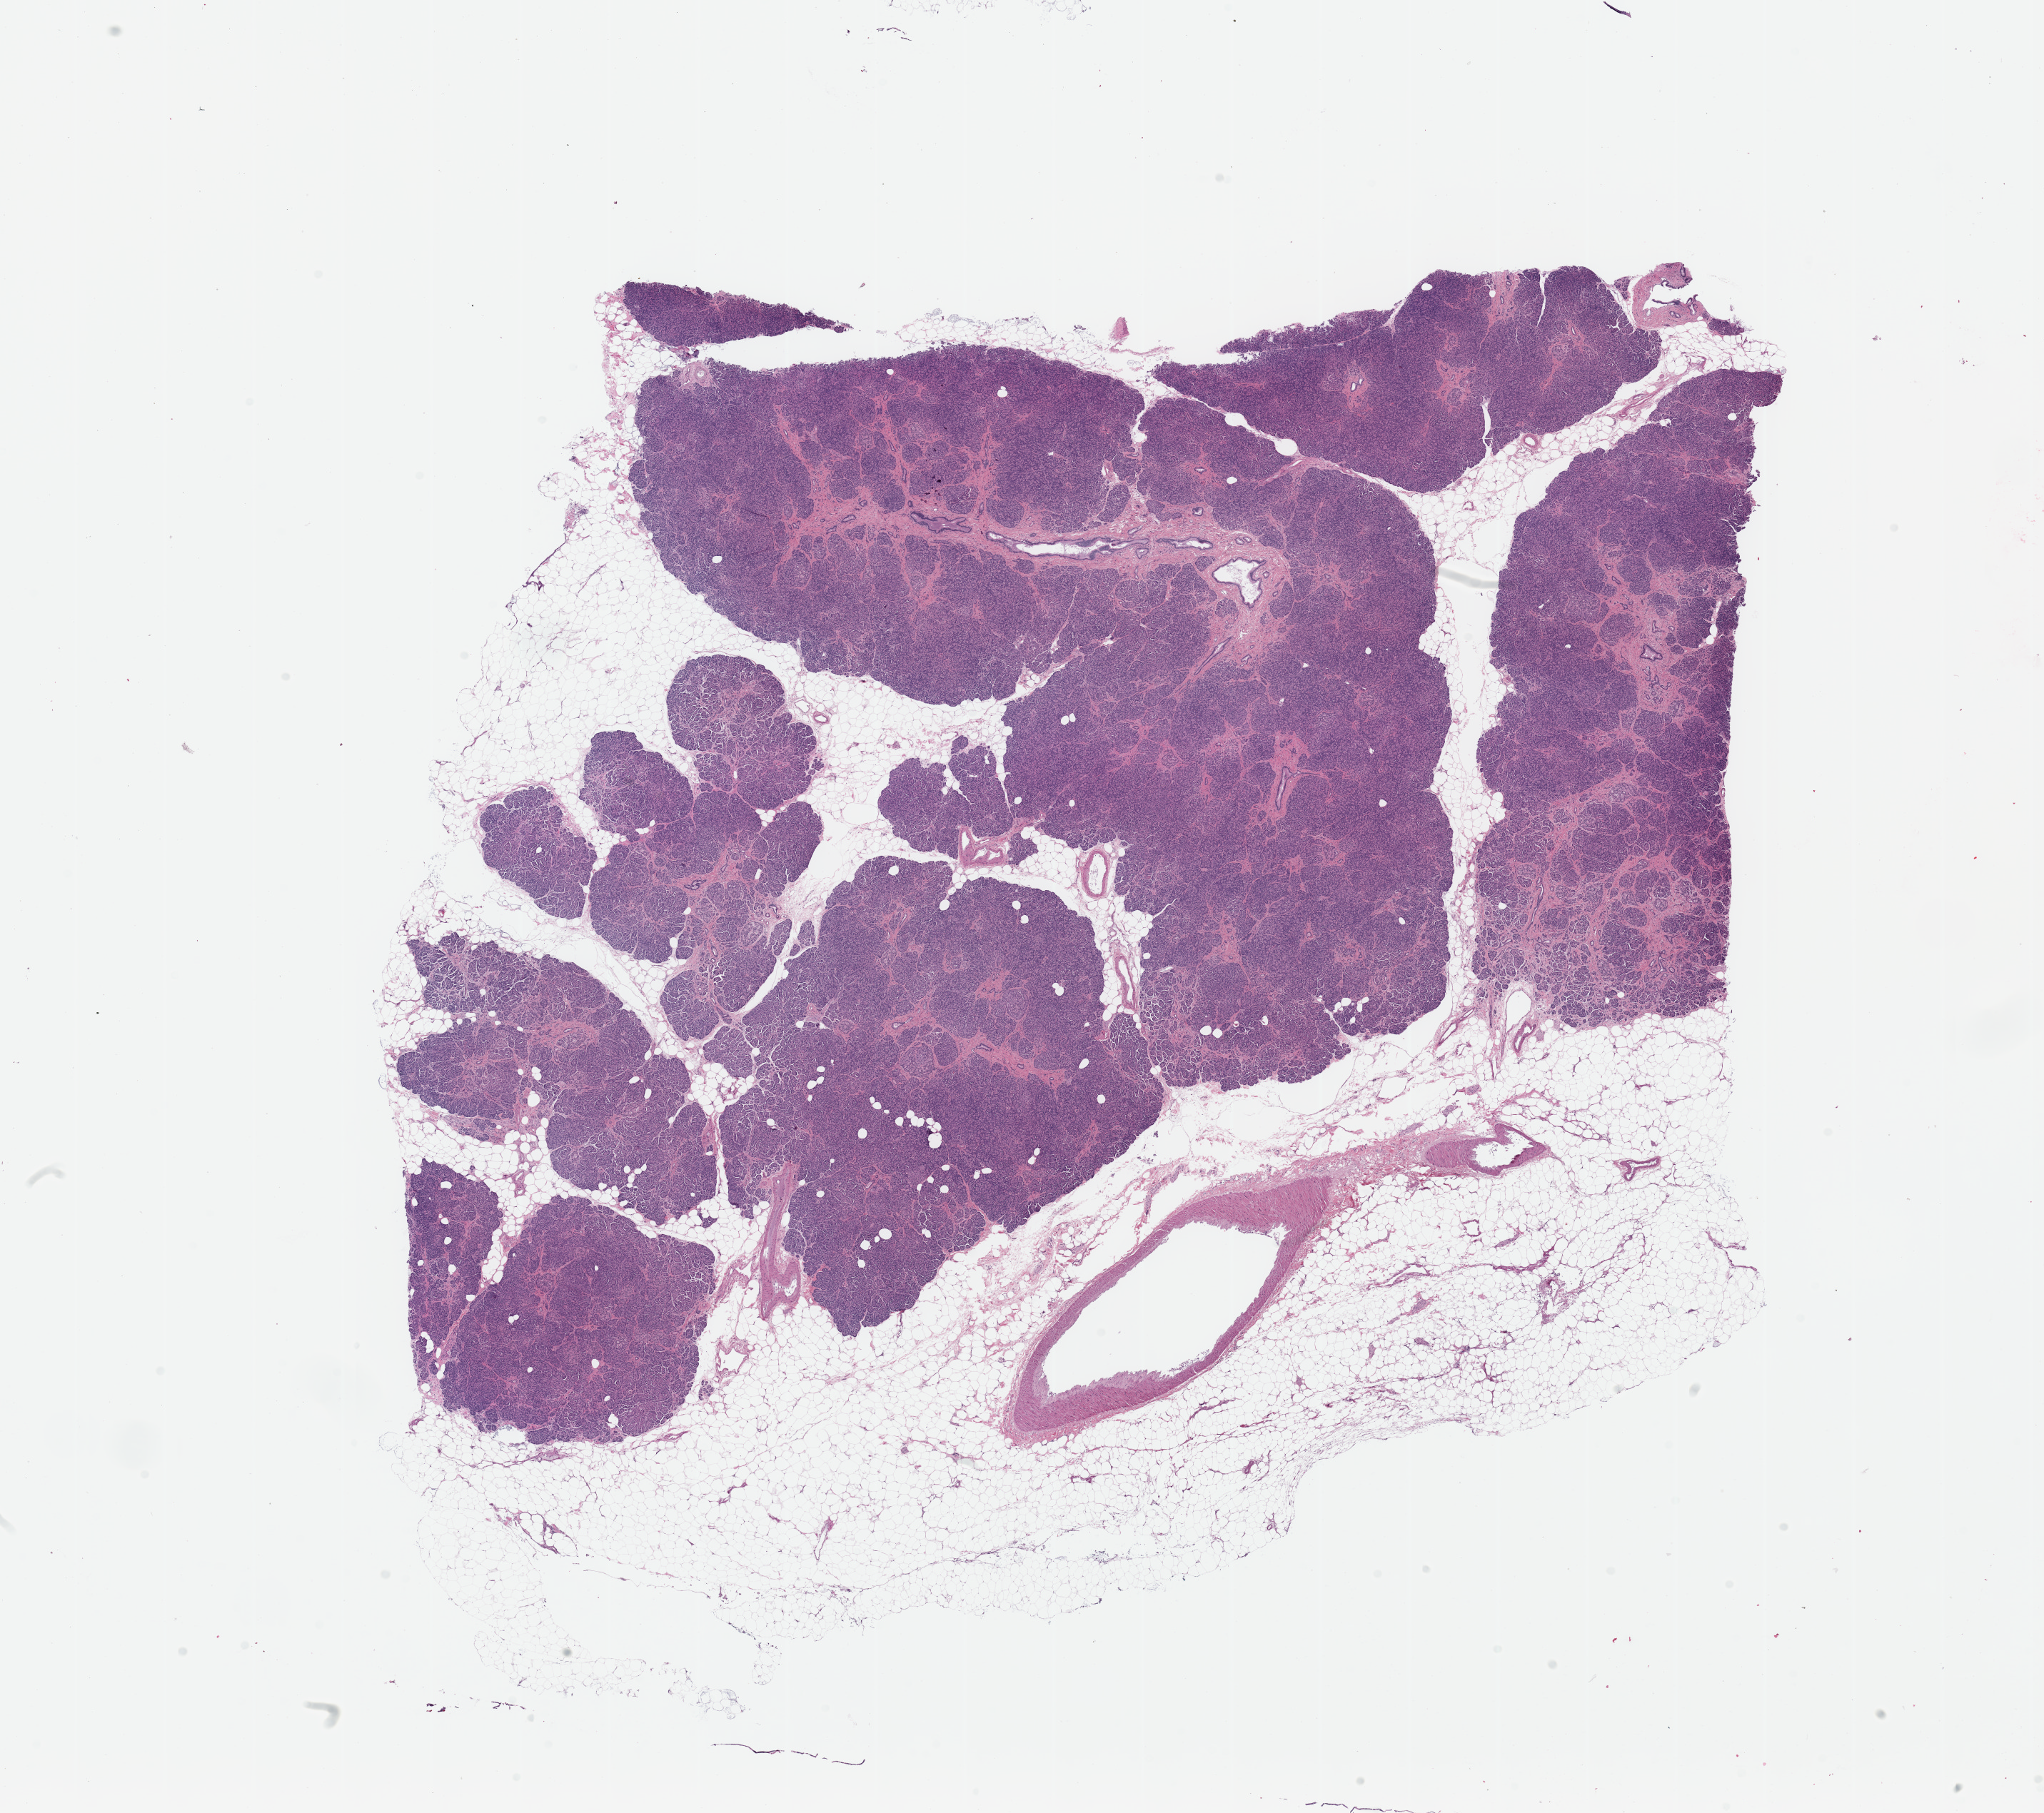
Digitized Hematoxylin and eosin (H&E) stained tissue section (whole slide) — low-resolution overview of the scanned area, about 22.6 x 20.1 mm; normal (non-tumour) tissue sample, sampled site: pancreas. Male, 64 y/o.
- this section: normal (non-tumour) tissue from the same patient
- patient diagnosis: Infiltrating duct carcinoma, NOS